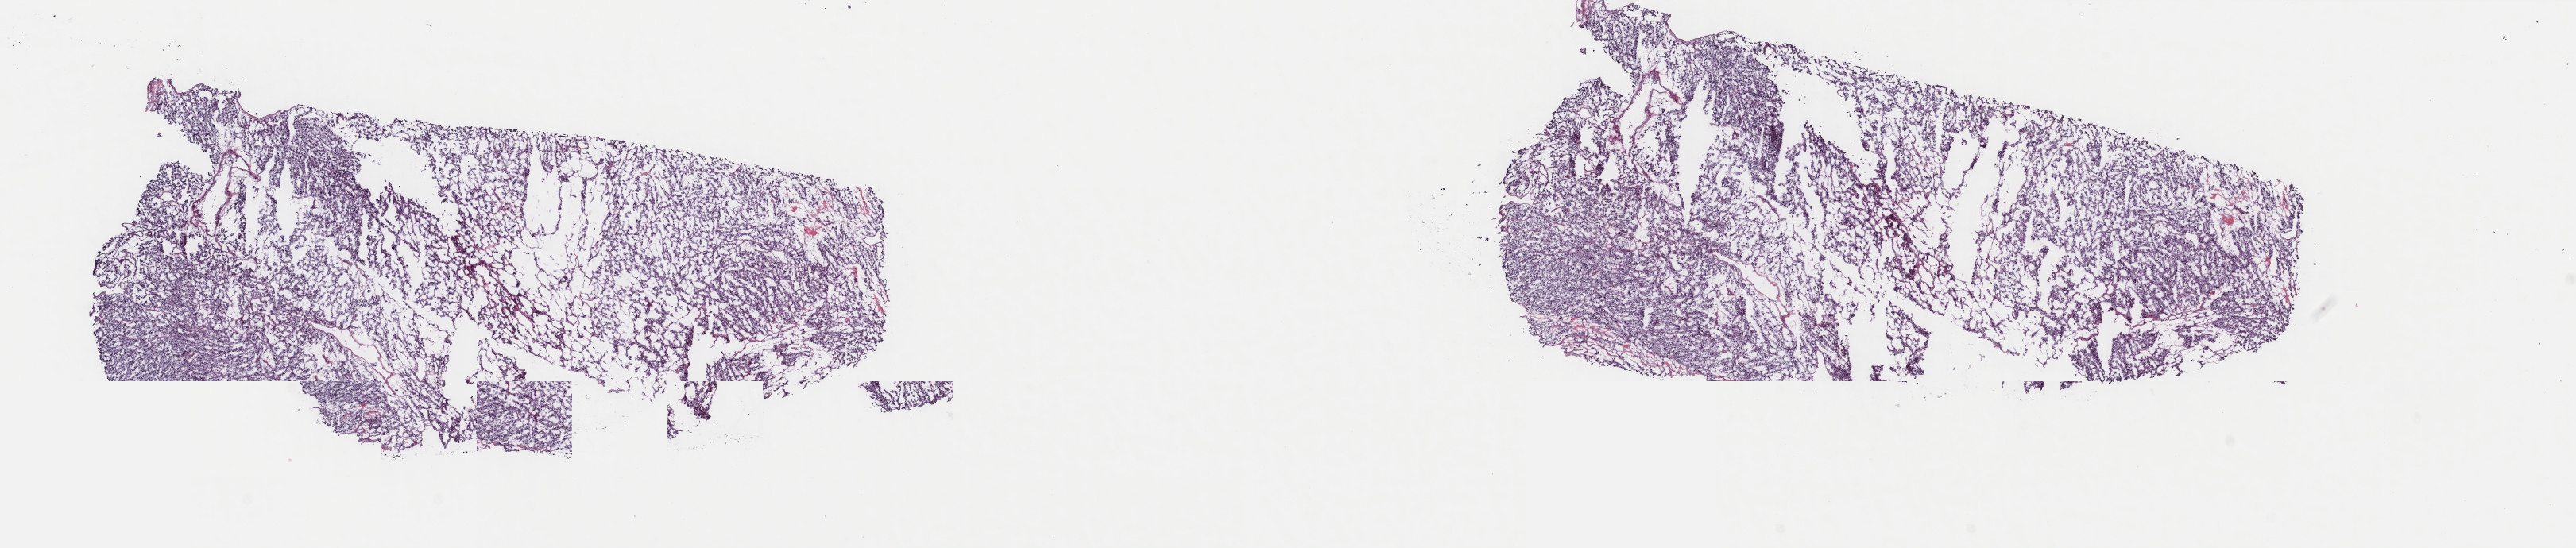
Whole-slide histology image, H&E, shown as a low-resolution overview of the whole scanned area (about 25.7 x 5.5 mm), frozen section, primary tumour sample from the adrenal gland. Male patient; age at initial diagnosis 43 years. Slide review estimates, as recorded: tumour cells 95%, tumour nuclei 100%, normal cells 0%, stromal cells 5%, necrosis 0%. Inflammatory infiltration, as recorded: lymphocyte infiltration 0%, monocyte infiltration 0%, neutrophil infiltration 0%.
Laterality: right. Histologic diagnosis: Pheochromocytoma, NOS.